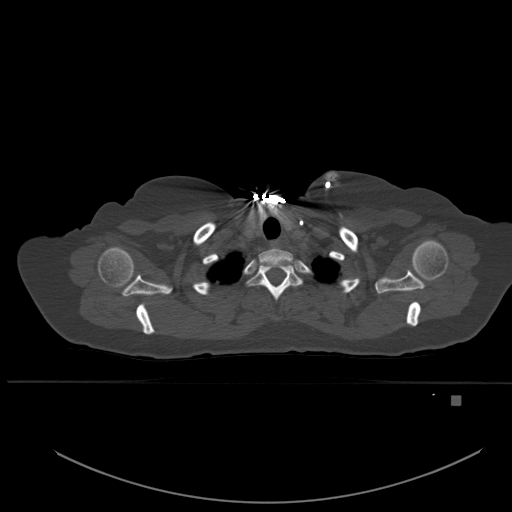
CT including the spine, one axial slice. Slice 420 of 651 in the series (ordered by position). Bone window (W 1800 / L 400 HU). 1.5 mm slice thickness. 512 × 512 image matrix, field of view 443 × 443 mm. Patient: female, 49 years. From the clinical record (not read from this slice): primary cancer: breast.
Outlined on this slice (semi-automatic segmentation, software-assisted and operator-edited):
- T1 vertebra: bounding box [x1, y1, x2, y2] px = [247, 263, 303, 300]